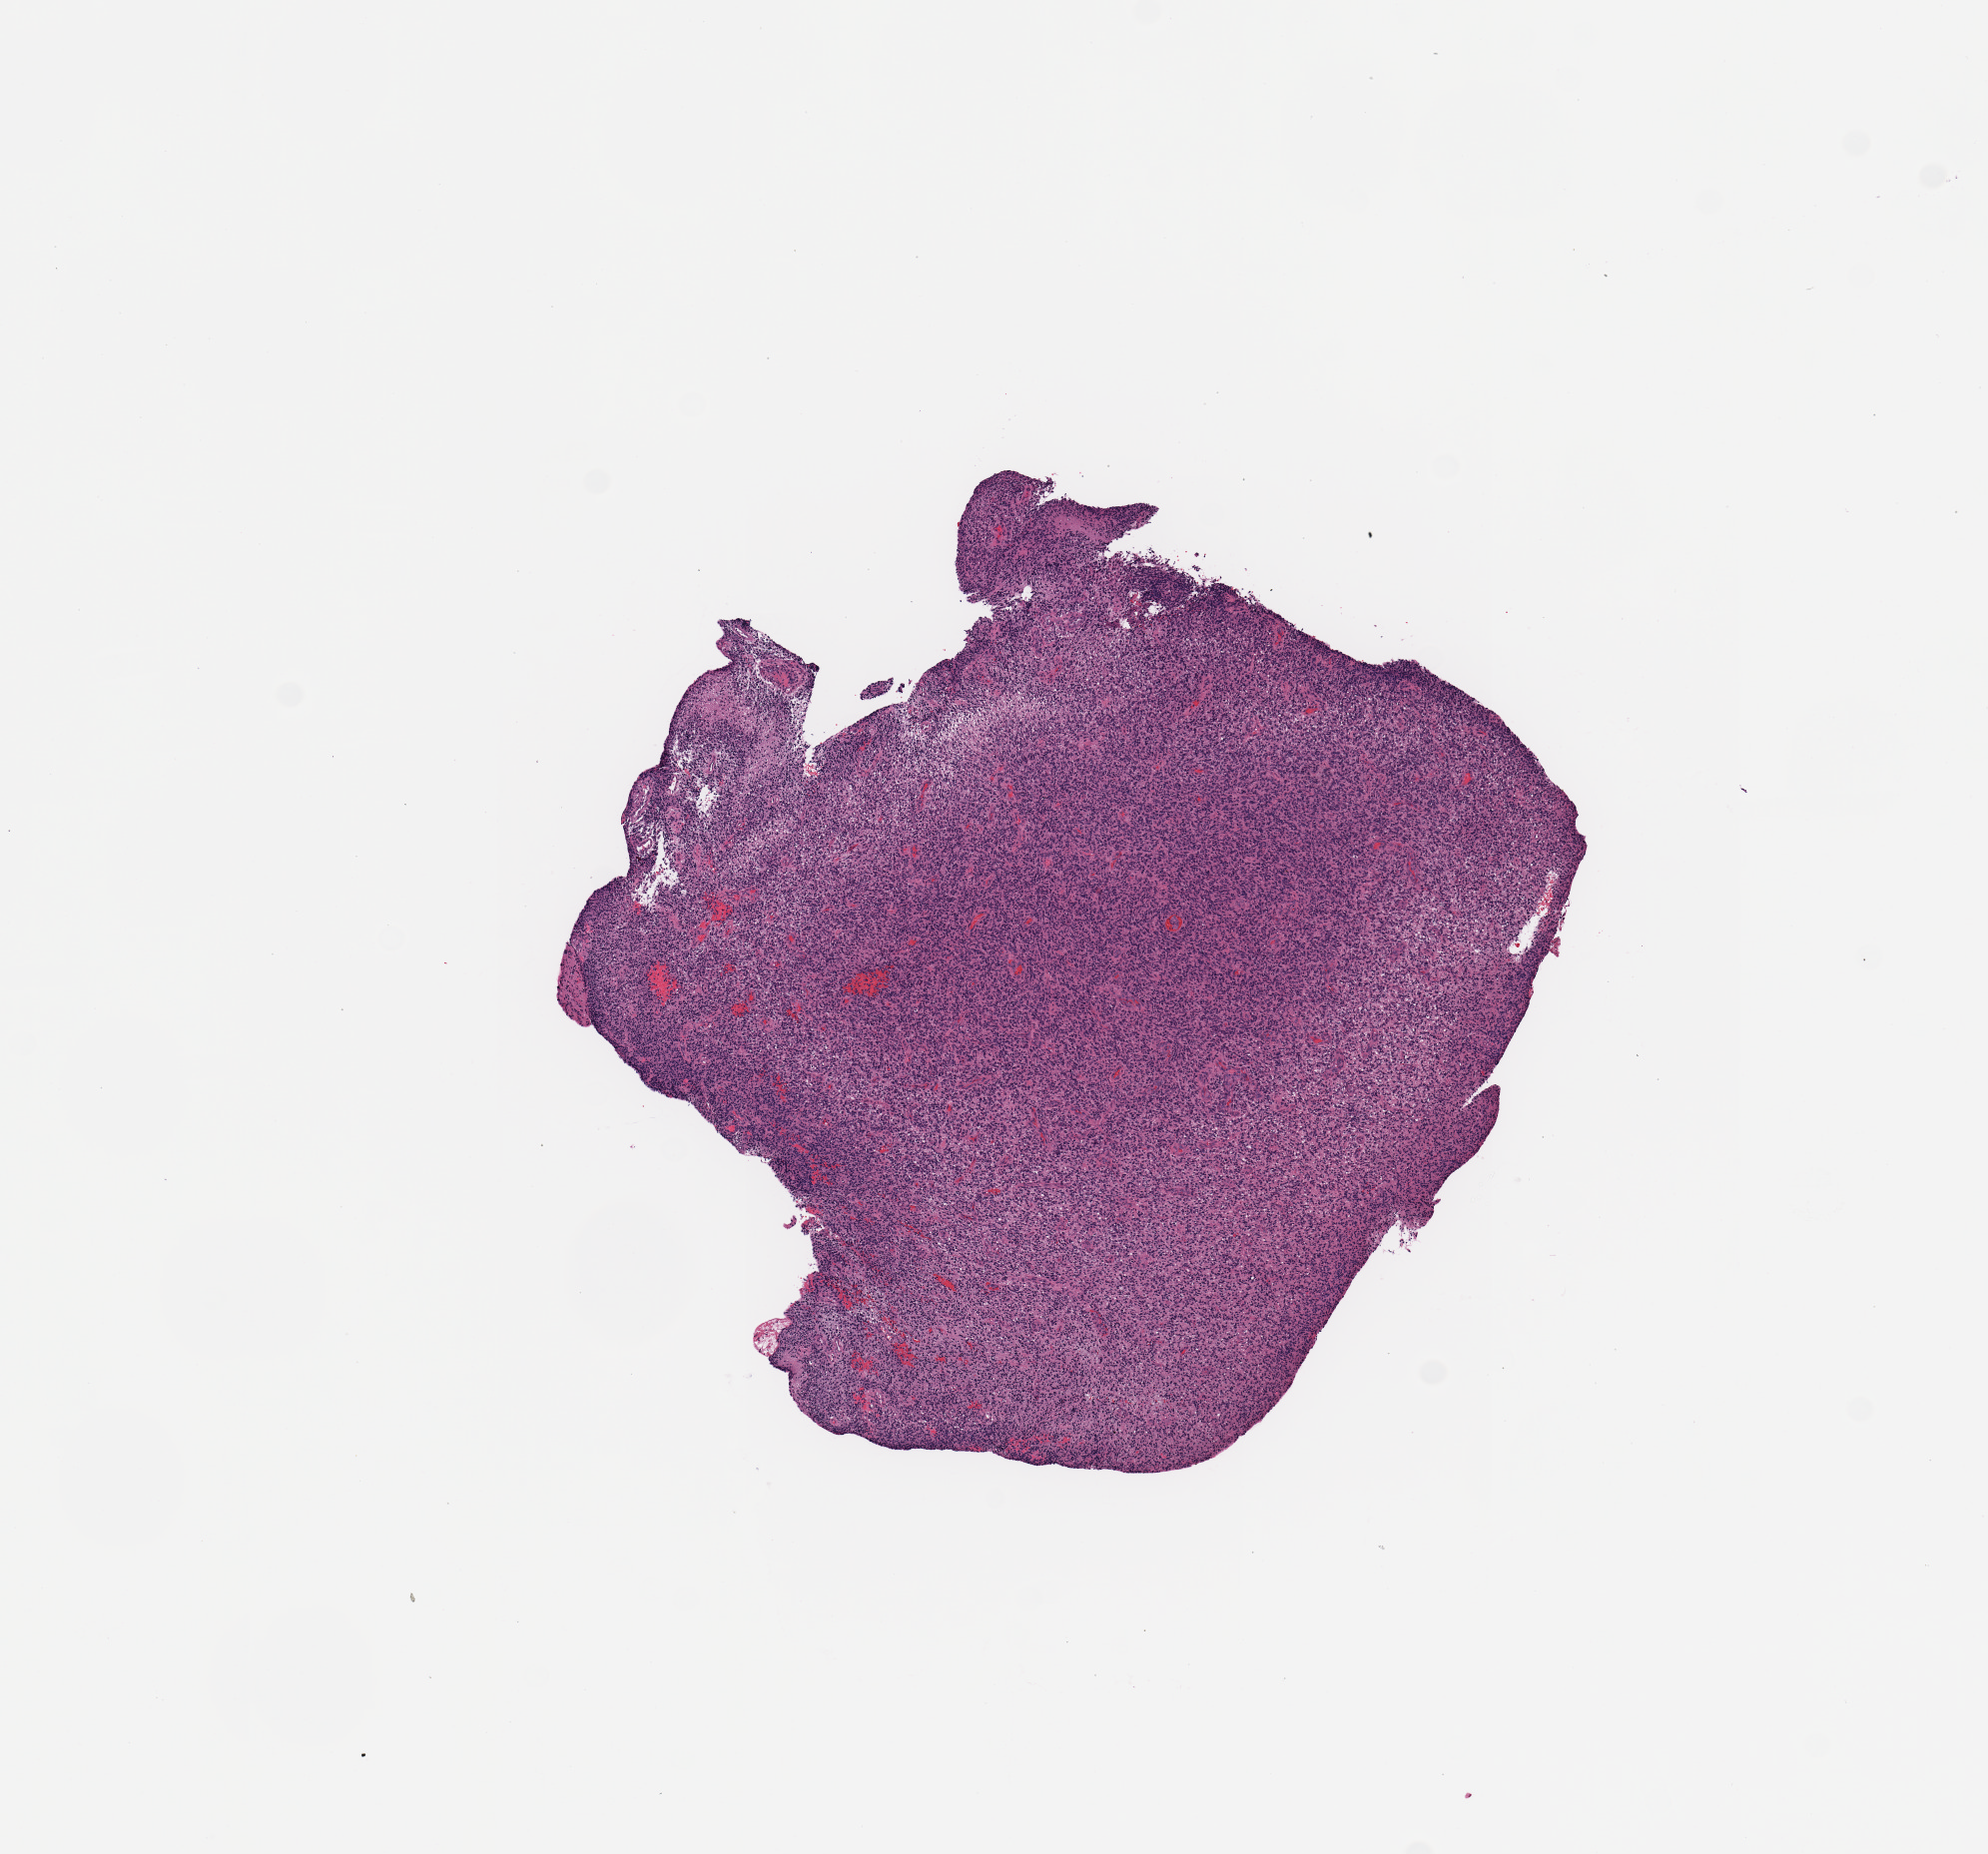
H&E-stained whole-slide image — a low-resolution overview of the entire scanned area, about 7.9 x 7.3 mm (from a 20x scan); tumour tissue sample, sampled site: brain. 44-year-old female patient. Pathologist review of this section (percent, as recorded): tumour nuclei 90%, necrosis 3%.
Diagnosis: Glioblastoma.